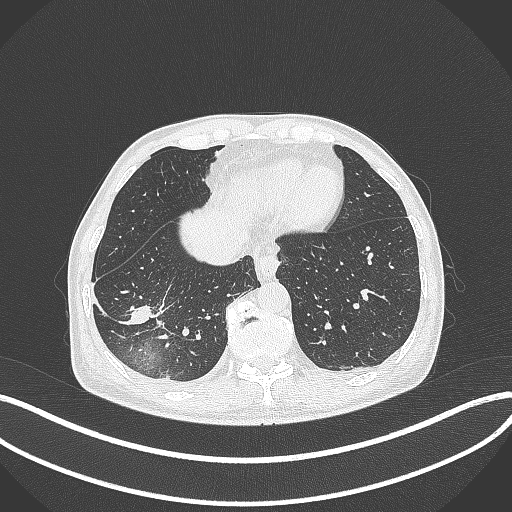
Chest CT, one axial slice. Slice 94 of 388 in the series (ordered by position). Reconstruction kernel B70f. 120 kVp. Lung window (W 1500 / L -600 HU). 1 mm slice thickness. 512 × 512 image matrix. Male patient, age 64 years. From the clinical record (not read from this slice): clinical TNM (as recorded): T3 N0 M0.
Structures marked on this image (bounding box drawn by a radiologist):
- lung tumour (recorded histology: adenocarcinoma): bounding box (x1, y1, x2, y2) in pixels: (125, 296, 174, 328)